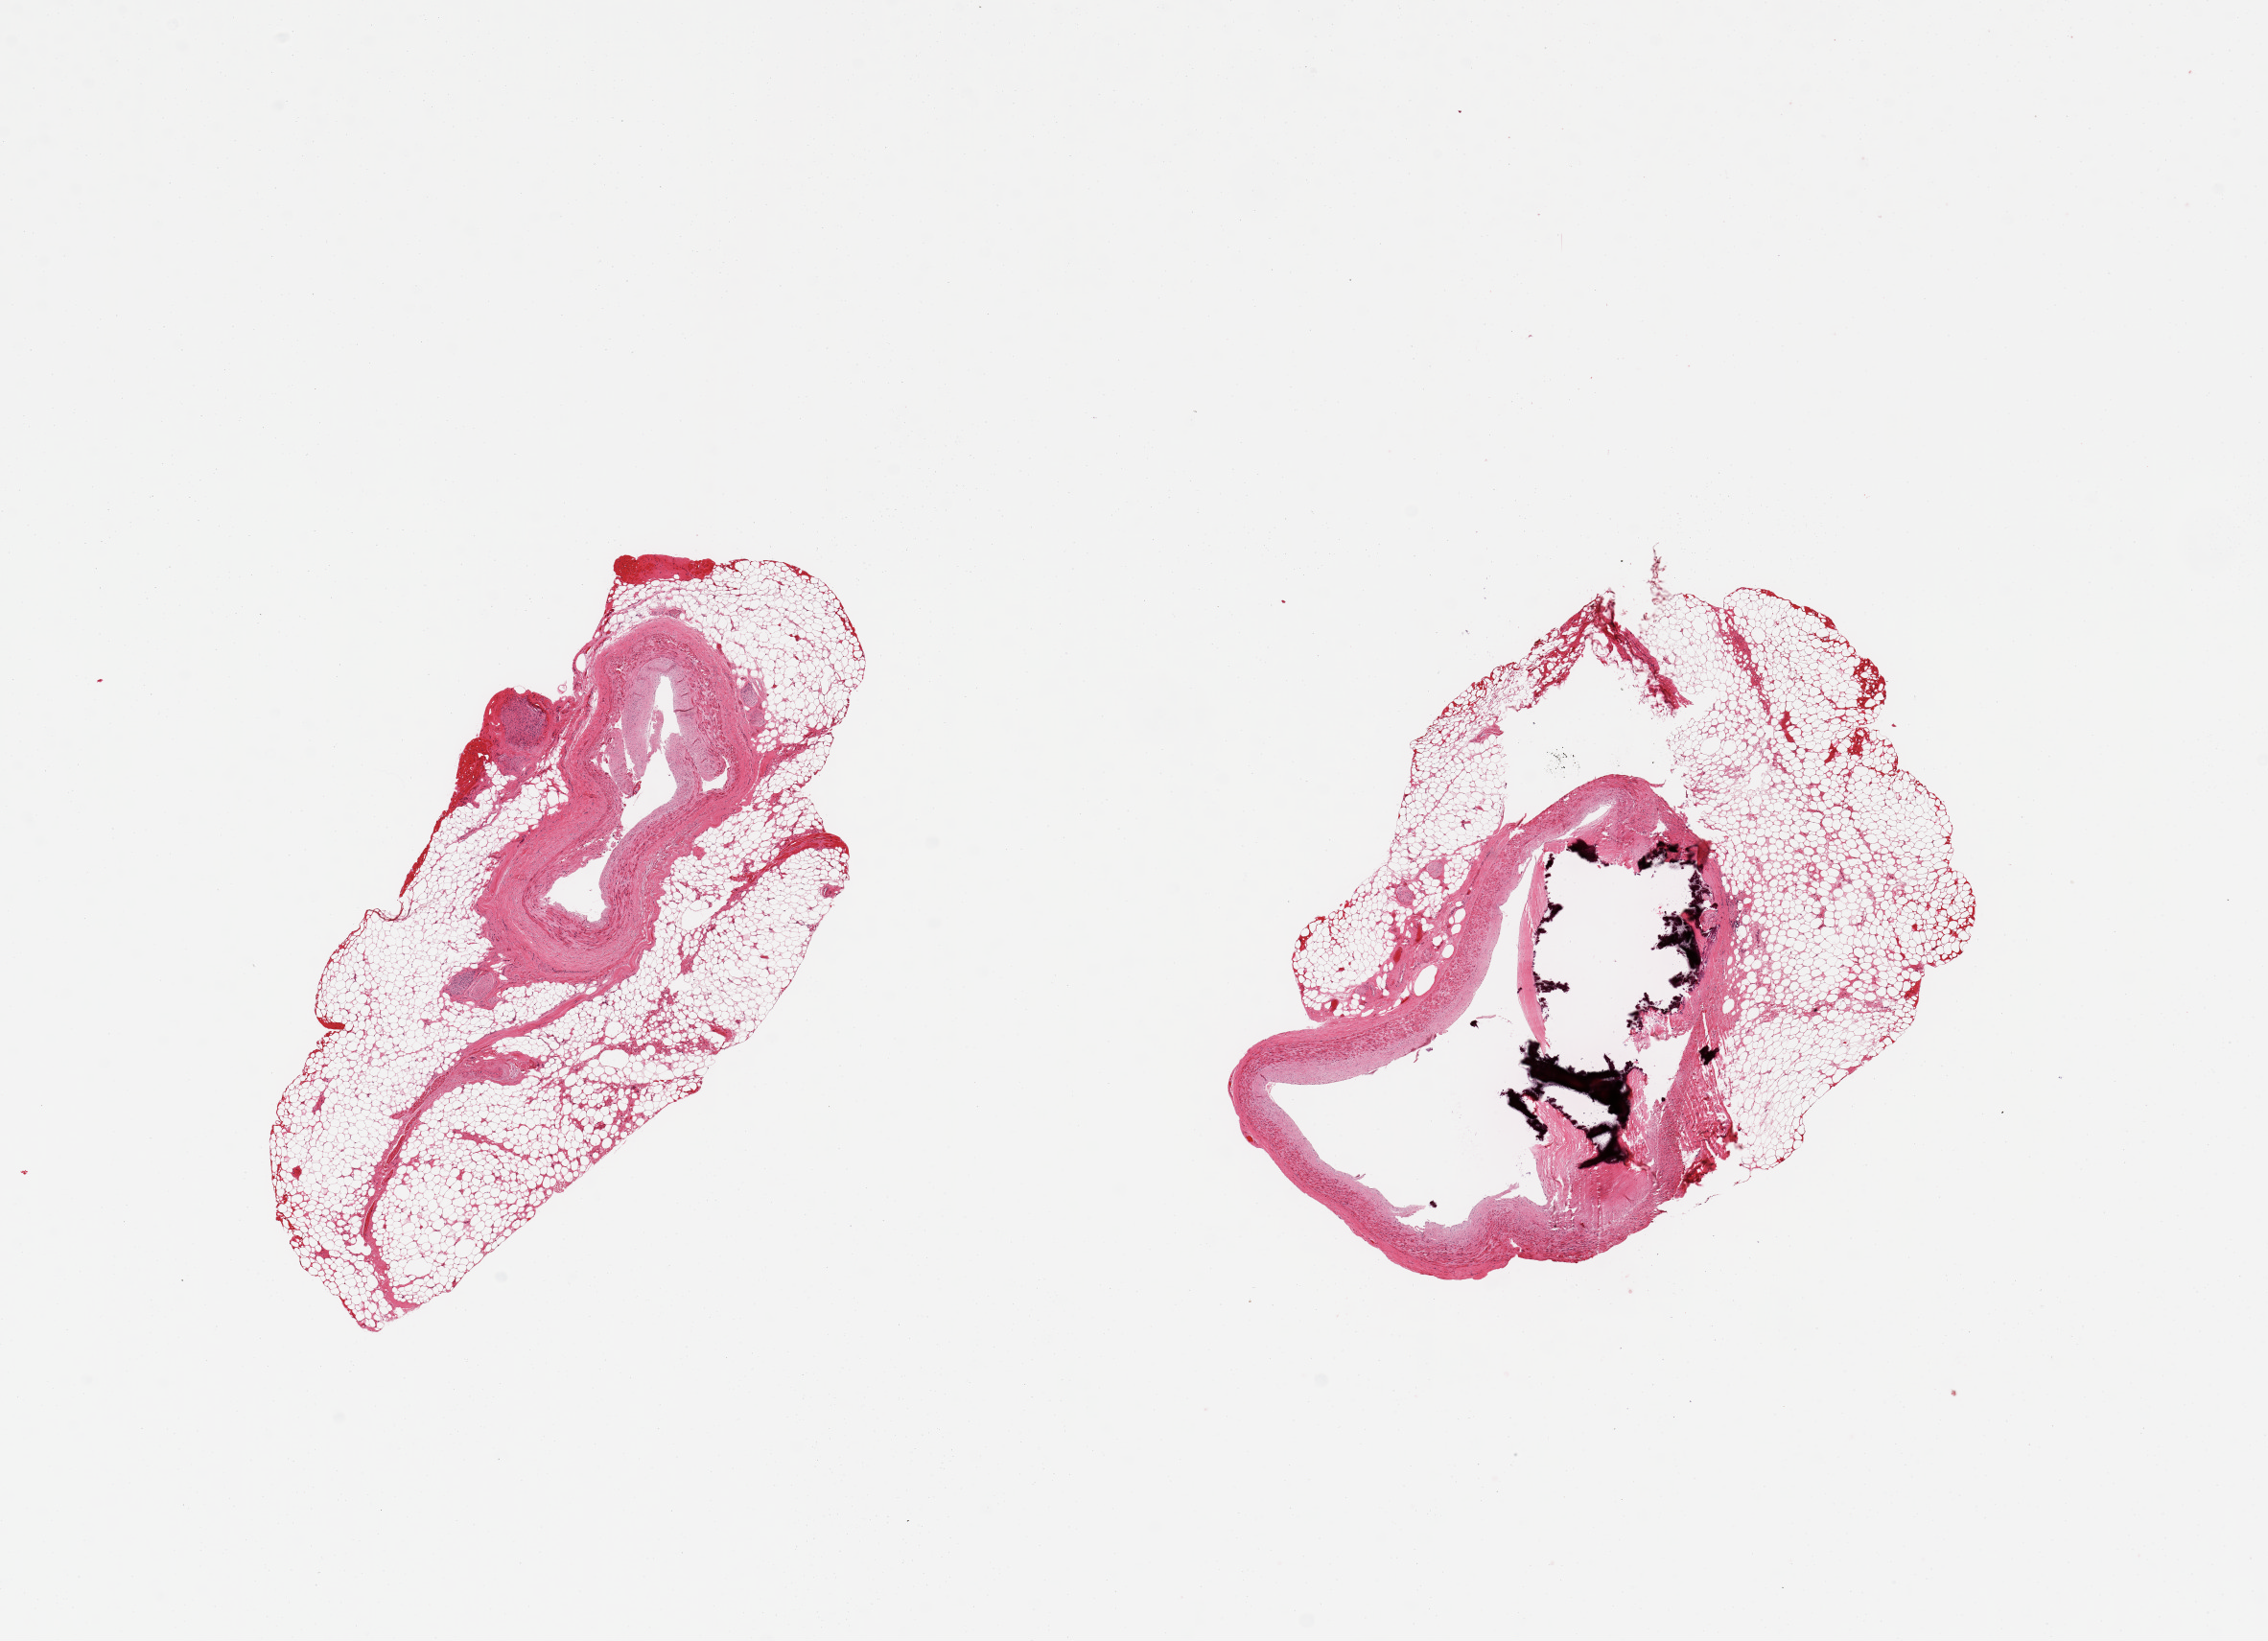
Digitized H&E-stained section, shown as a low-resolution overview of the whole scanned area (about 18.7 x 13.5 mm, slide scanned at 20x); PAXgene-fixed, paraffin-embedded tissue; section of coronary artery (target tissue); tissue donor sample. Male donor.
• reviewer comment on this tissue sample: 2 pieces; large calcific deposit in 1 piece; excessive perivascular extraneous fat over 60%